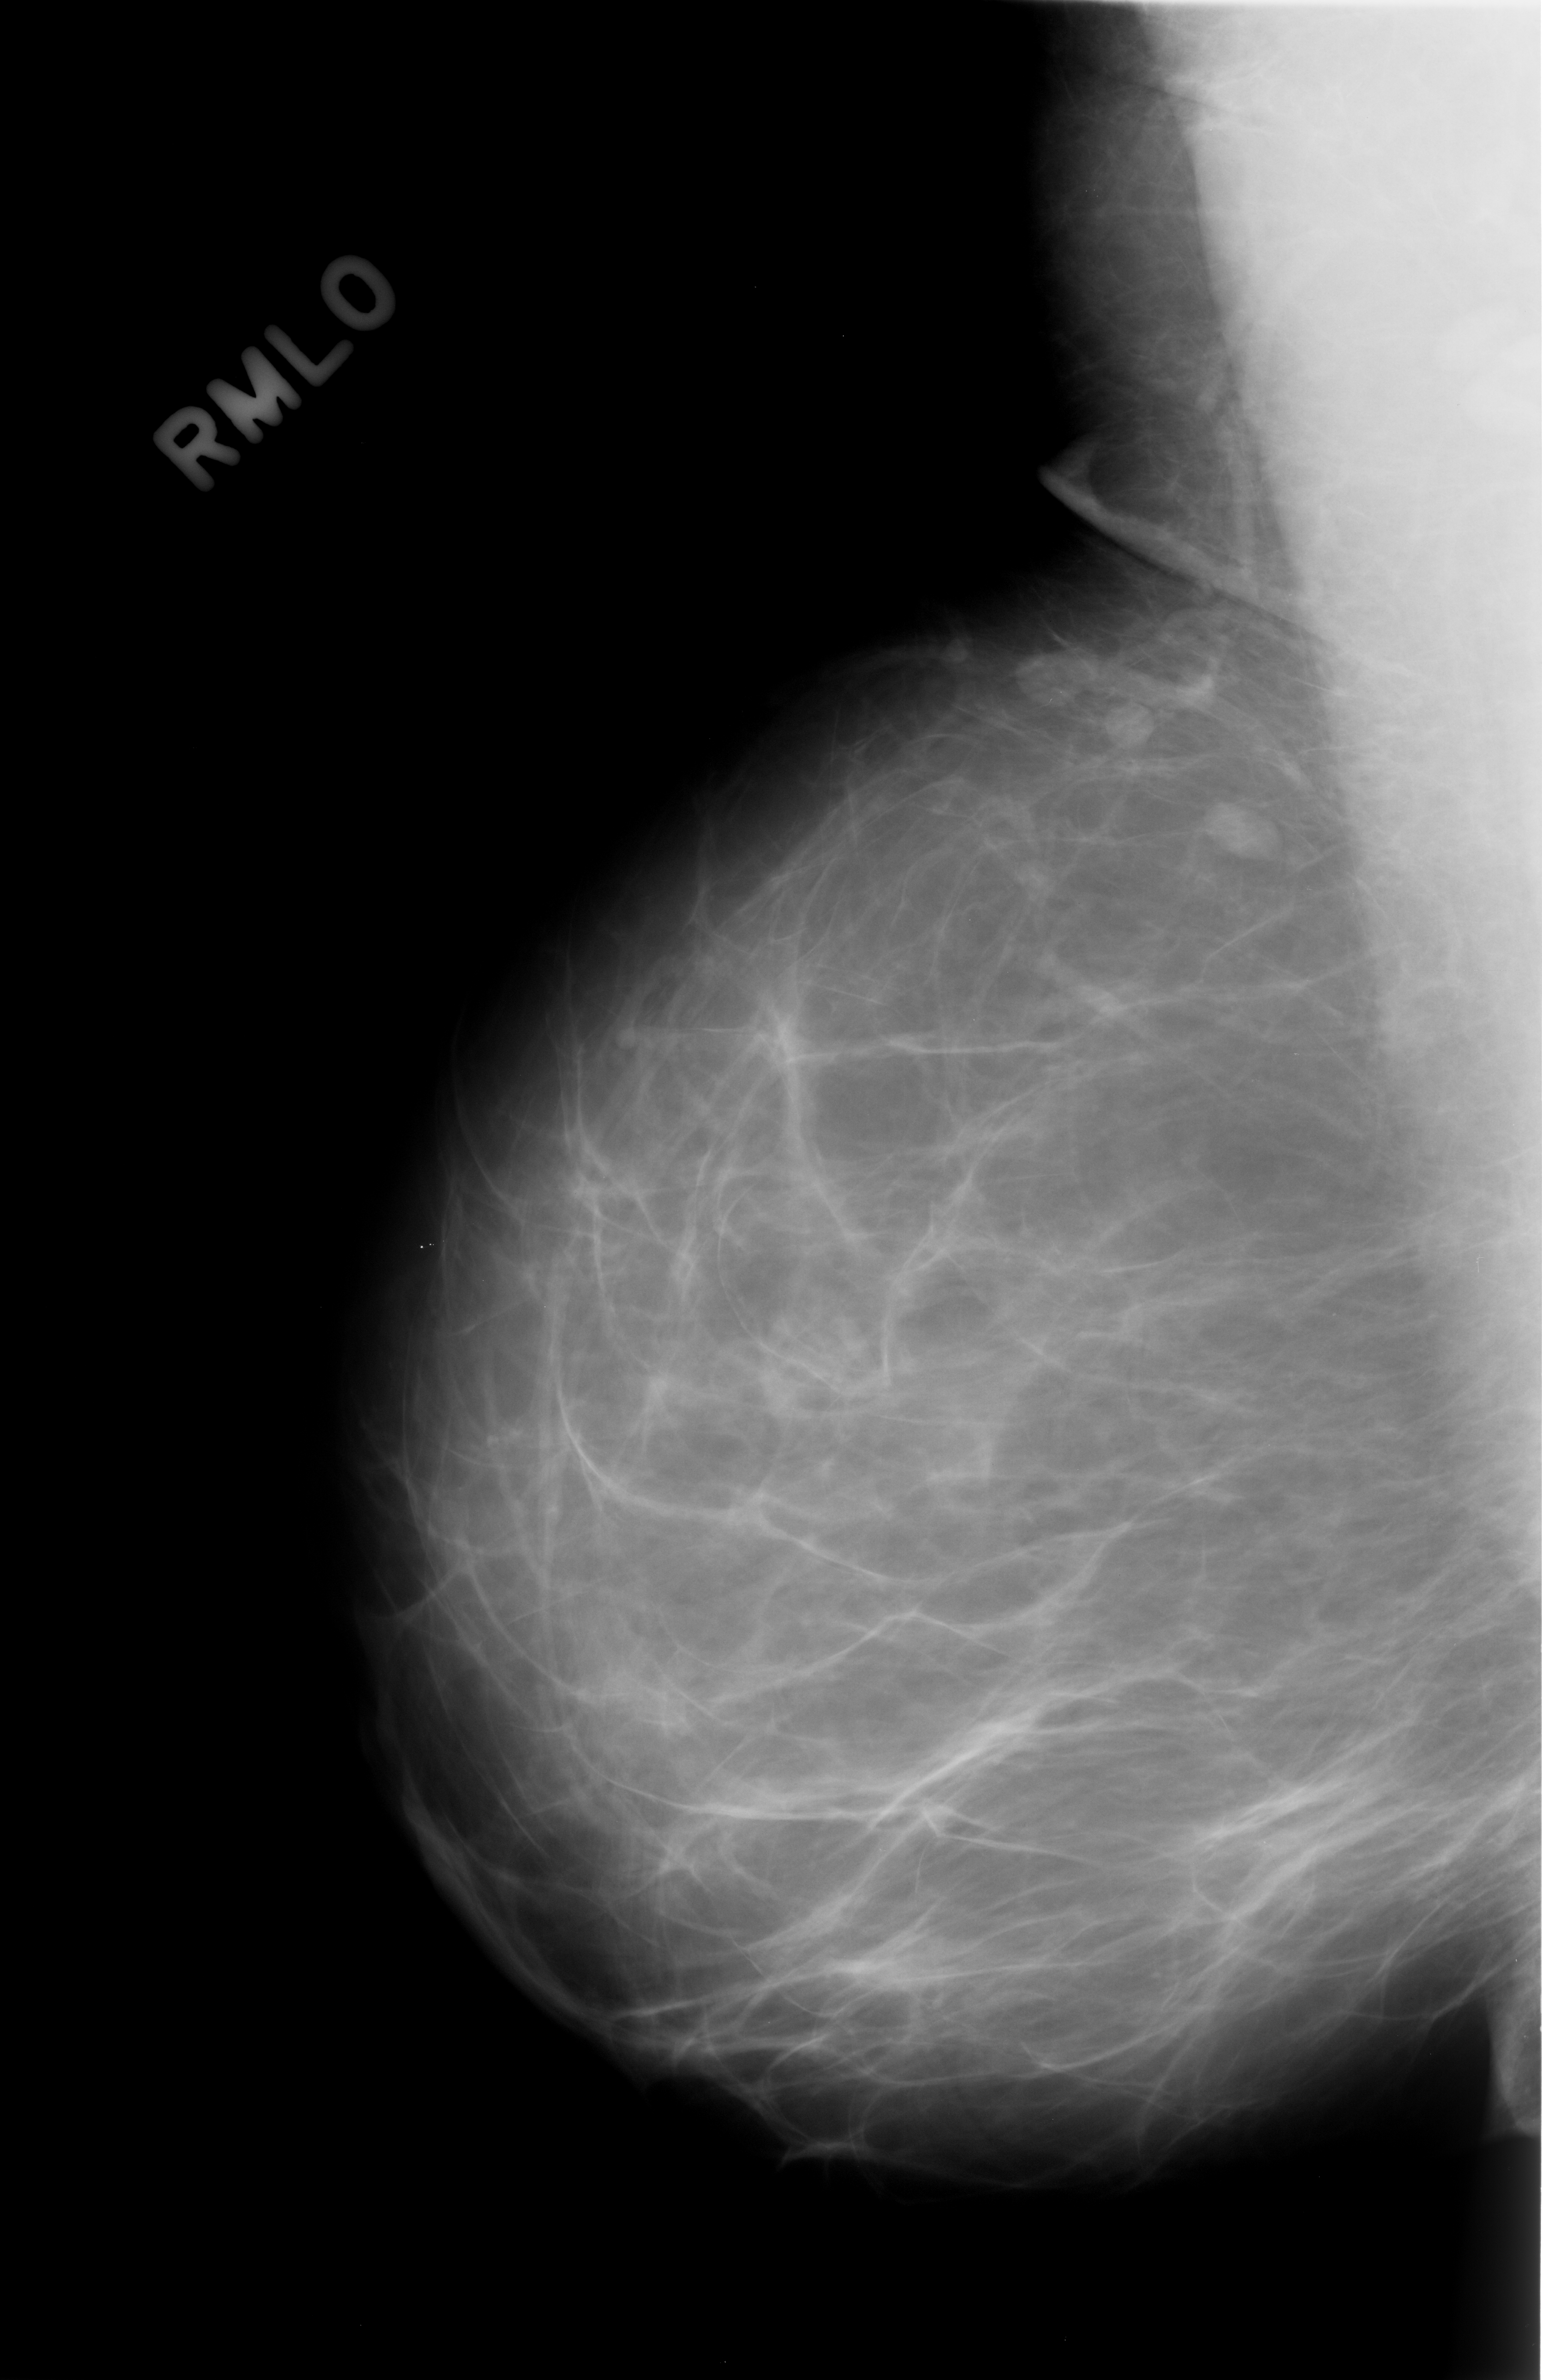
Mammogram (digitized film), right breast, MLO view, breast composition: almost entirely fatty (BI-RADS density category 1 of 4).
- Abnormality record for this image: Finding 1 of 3: mass, shape lobulated, margins circumscribed; BI-RADS assessment category 3; benign; no additional work-up was recommended (benign without callback).
- Finding 2 of 3: mass, shape round, margins circumscribed; BI-RADS assessment category 3; benign; no additional work-up was recommended (benign without callback).
- Finding 3 of 3: mass, shape oval, margins circumscribed; BI-RADS assessment category 3; benign; no additional work-up was recommended (benign without callback).